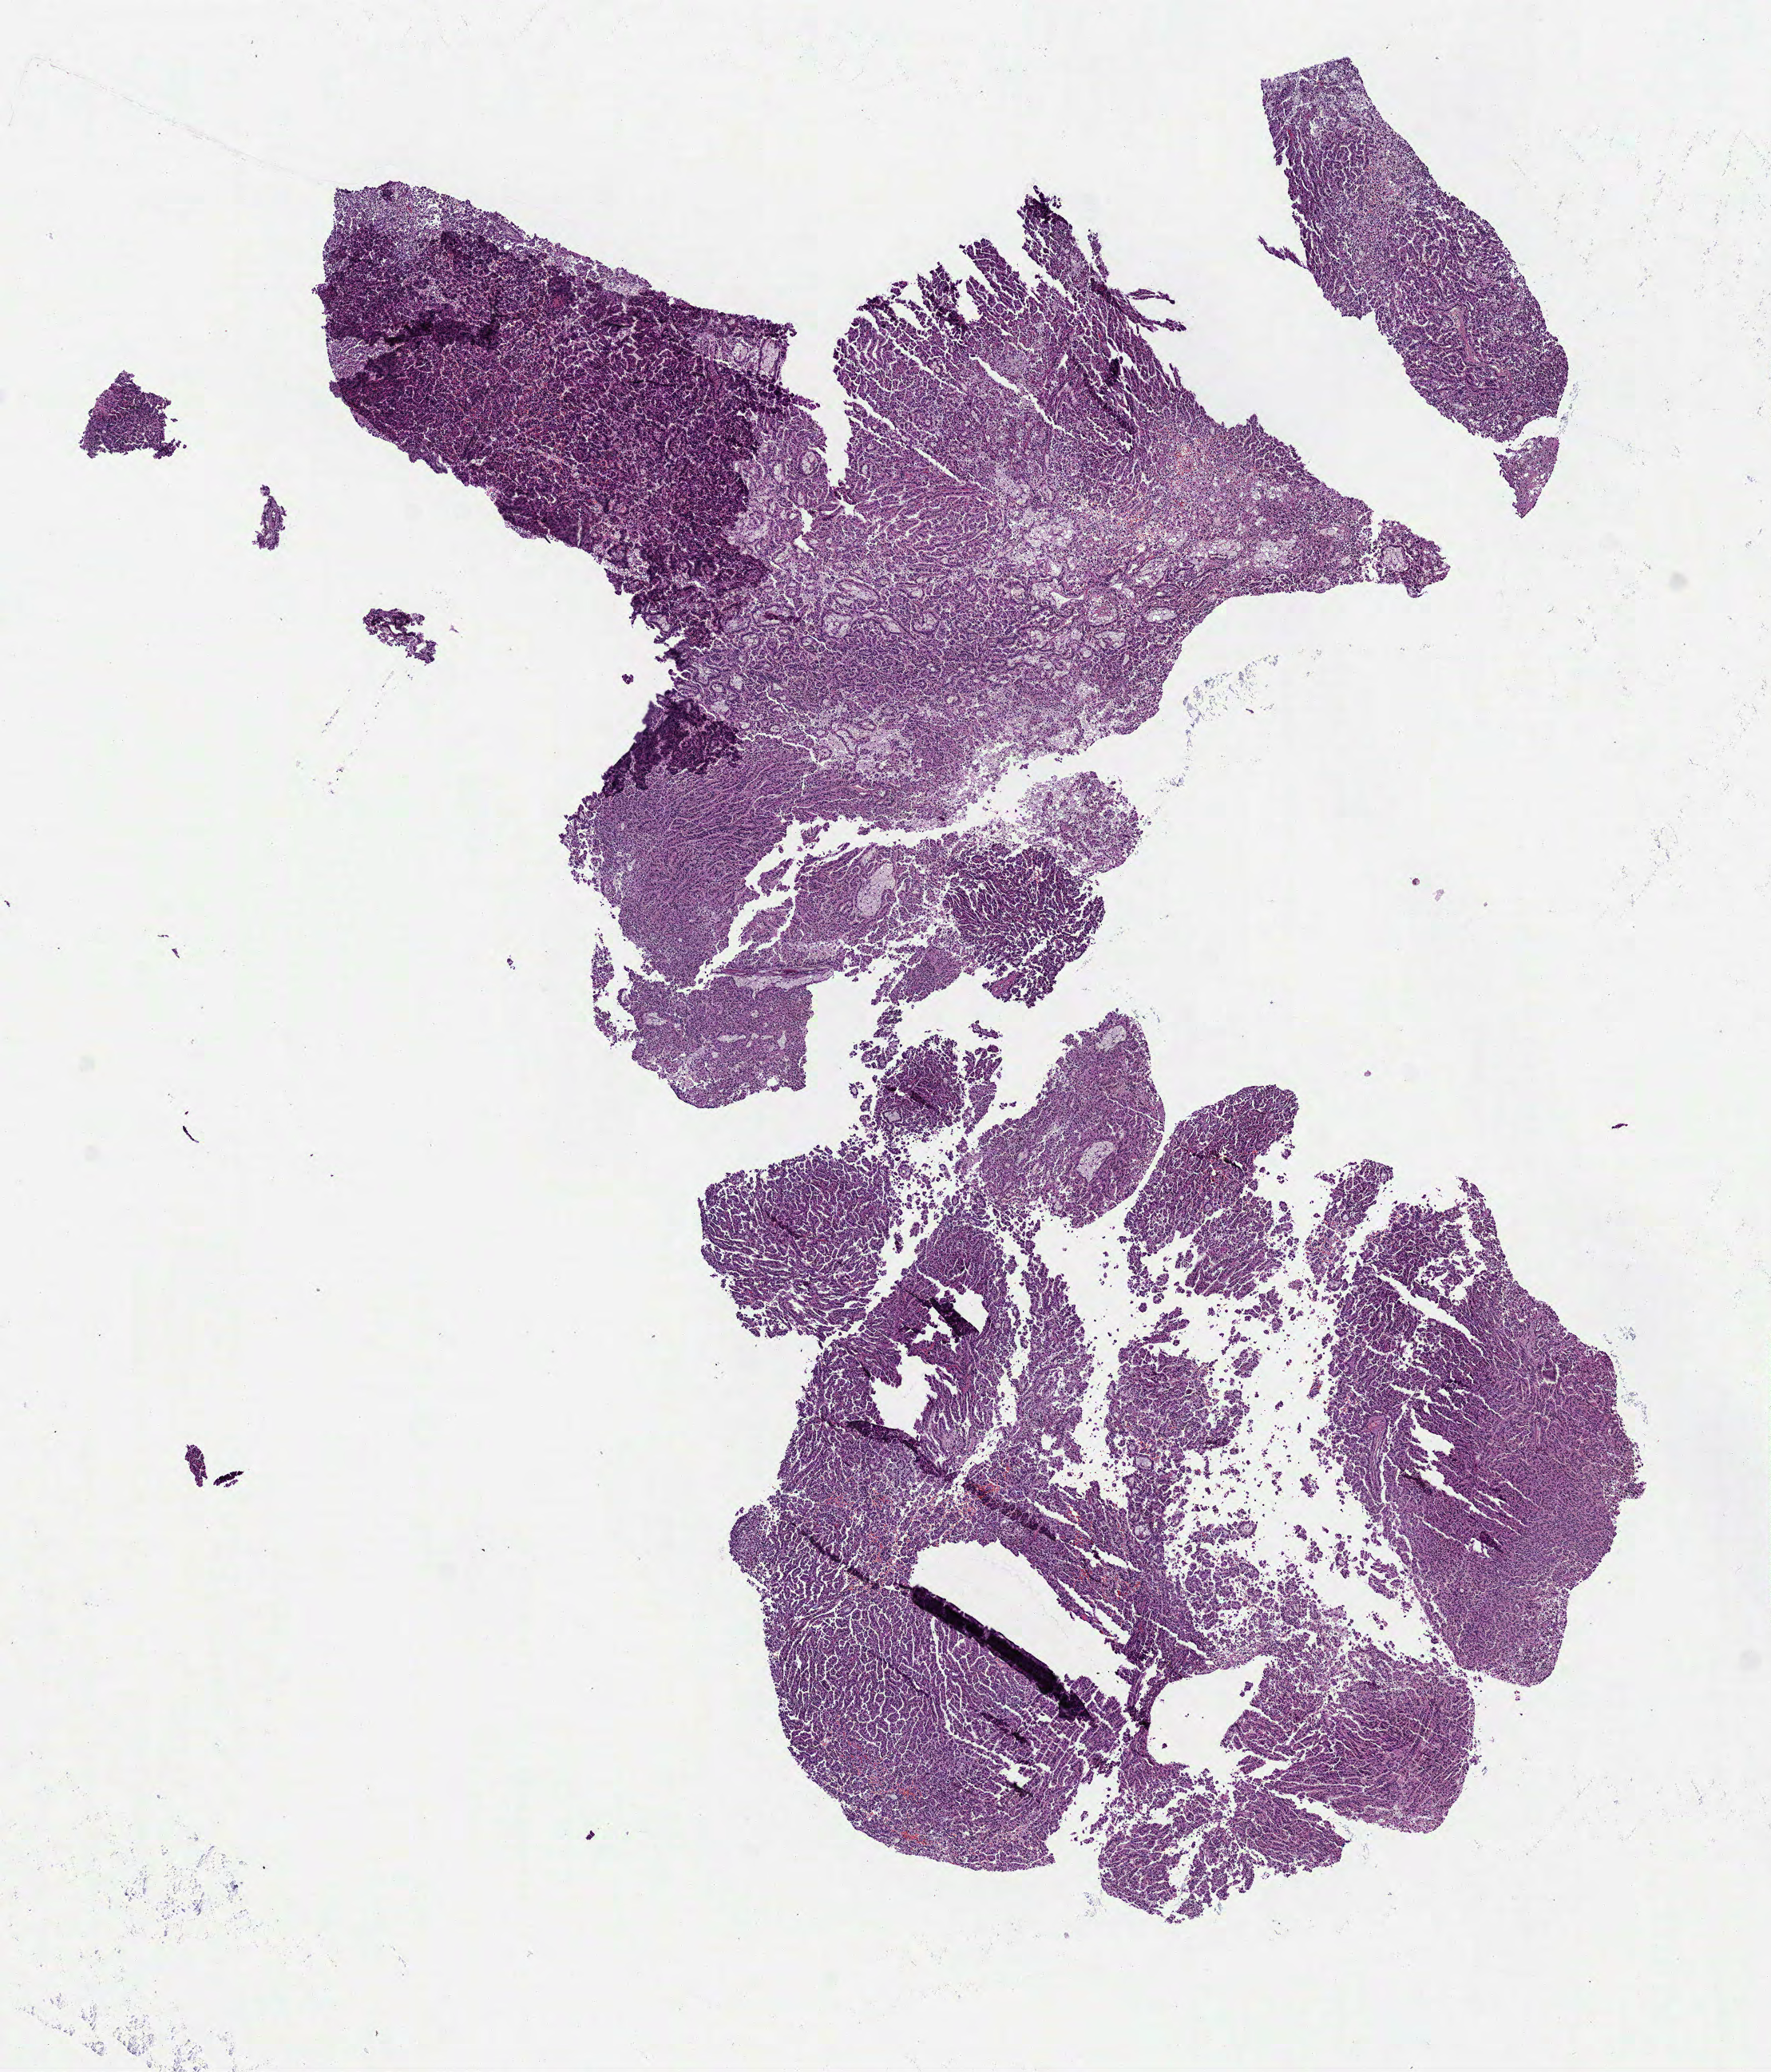
H&E whole-slide image, shown as a low-resolution overview of the whole scanned area (about 8.9 x 10.5 mm), FFPE section, primary tumour sample from the kidney. Female patient; age at initial diagnosis 45 years.
AJCC pathologic stage: I (7th edition). Diagnosis: Papillary adenocarcinoma, NOS. Laterality: left. TNM: T1a NX MX.